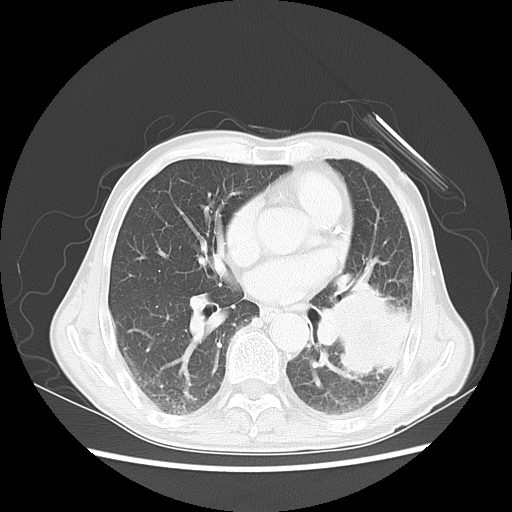
Chest CT, one axial slice. Position 25 of 51 along the scan axis. Reconstruction kernel LUNG. Lung window (W 1500 / L -600 HU). 5 mm slice thickness. 512 × 512 image matrix. Patient: male, 64 years. From the clinical record (not read from this slice): clinical TNM (as recorded): T4 N0 M0; histopathological grade: G2-3.
Structures marked on this image (rectangle marked by the reading radiologist):
- lung tumour (recorded histology: squamous cell carcinoma): bounding box (x1, y1, x2, y2) in pixels: (306, 268, 403, 385)